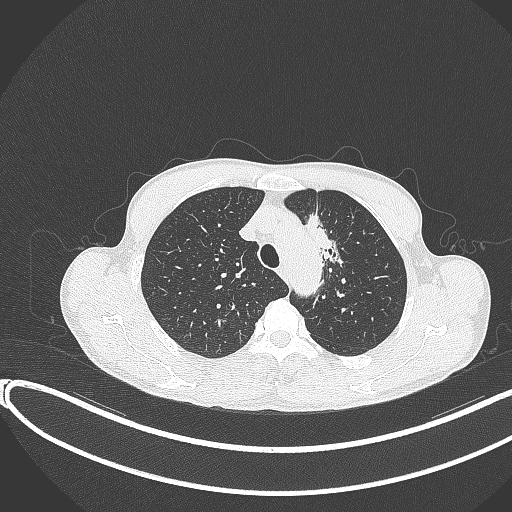
Chest CT, one axial slice; position 298 of 374 along the scan axis; 120 kVp; lung window (W 1500 / L -600 HU); 1 mm slice thickness; 512 × 512 image matrix. Patient: male, 58 years. Case-level facts recorded for this patient, not image findings: clinical TNM (as recorded): T1c N1 M0.
Outlined on this slice (rectangle marked by the reading radiologist):
- lung tumour (recorded histology: adenocarcinoma): bounding box (x1, y1, x2, y2) in pixels: (292, 212, 344, 276)